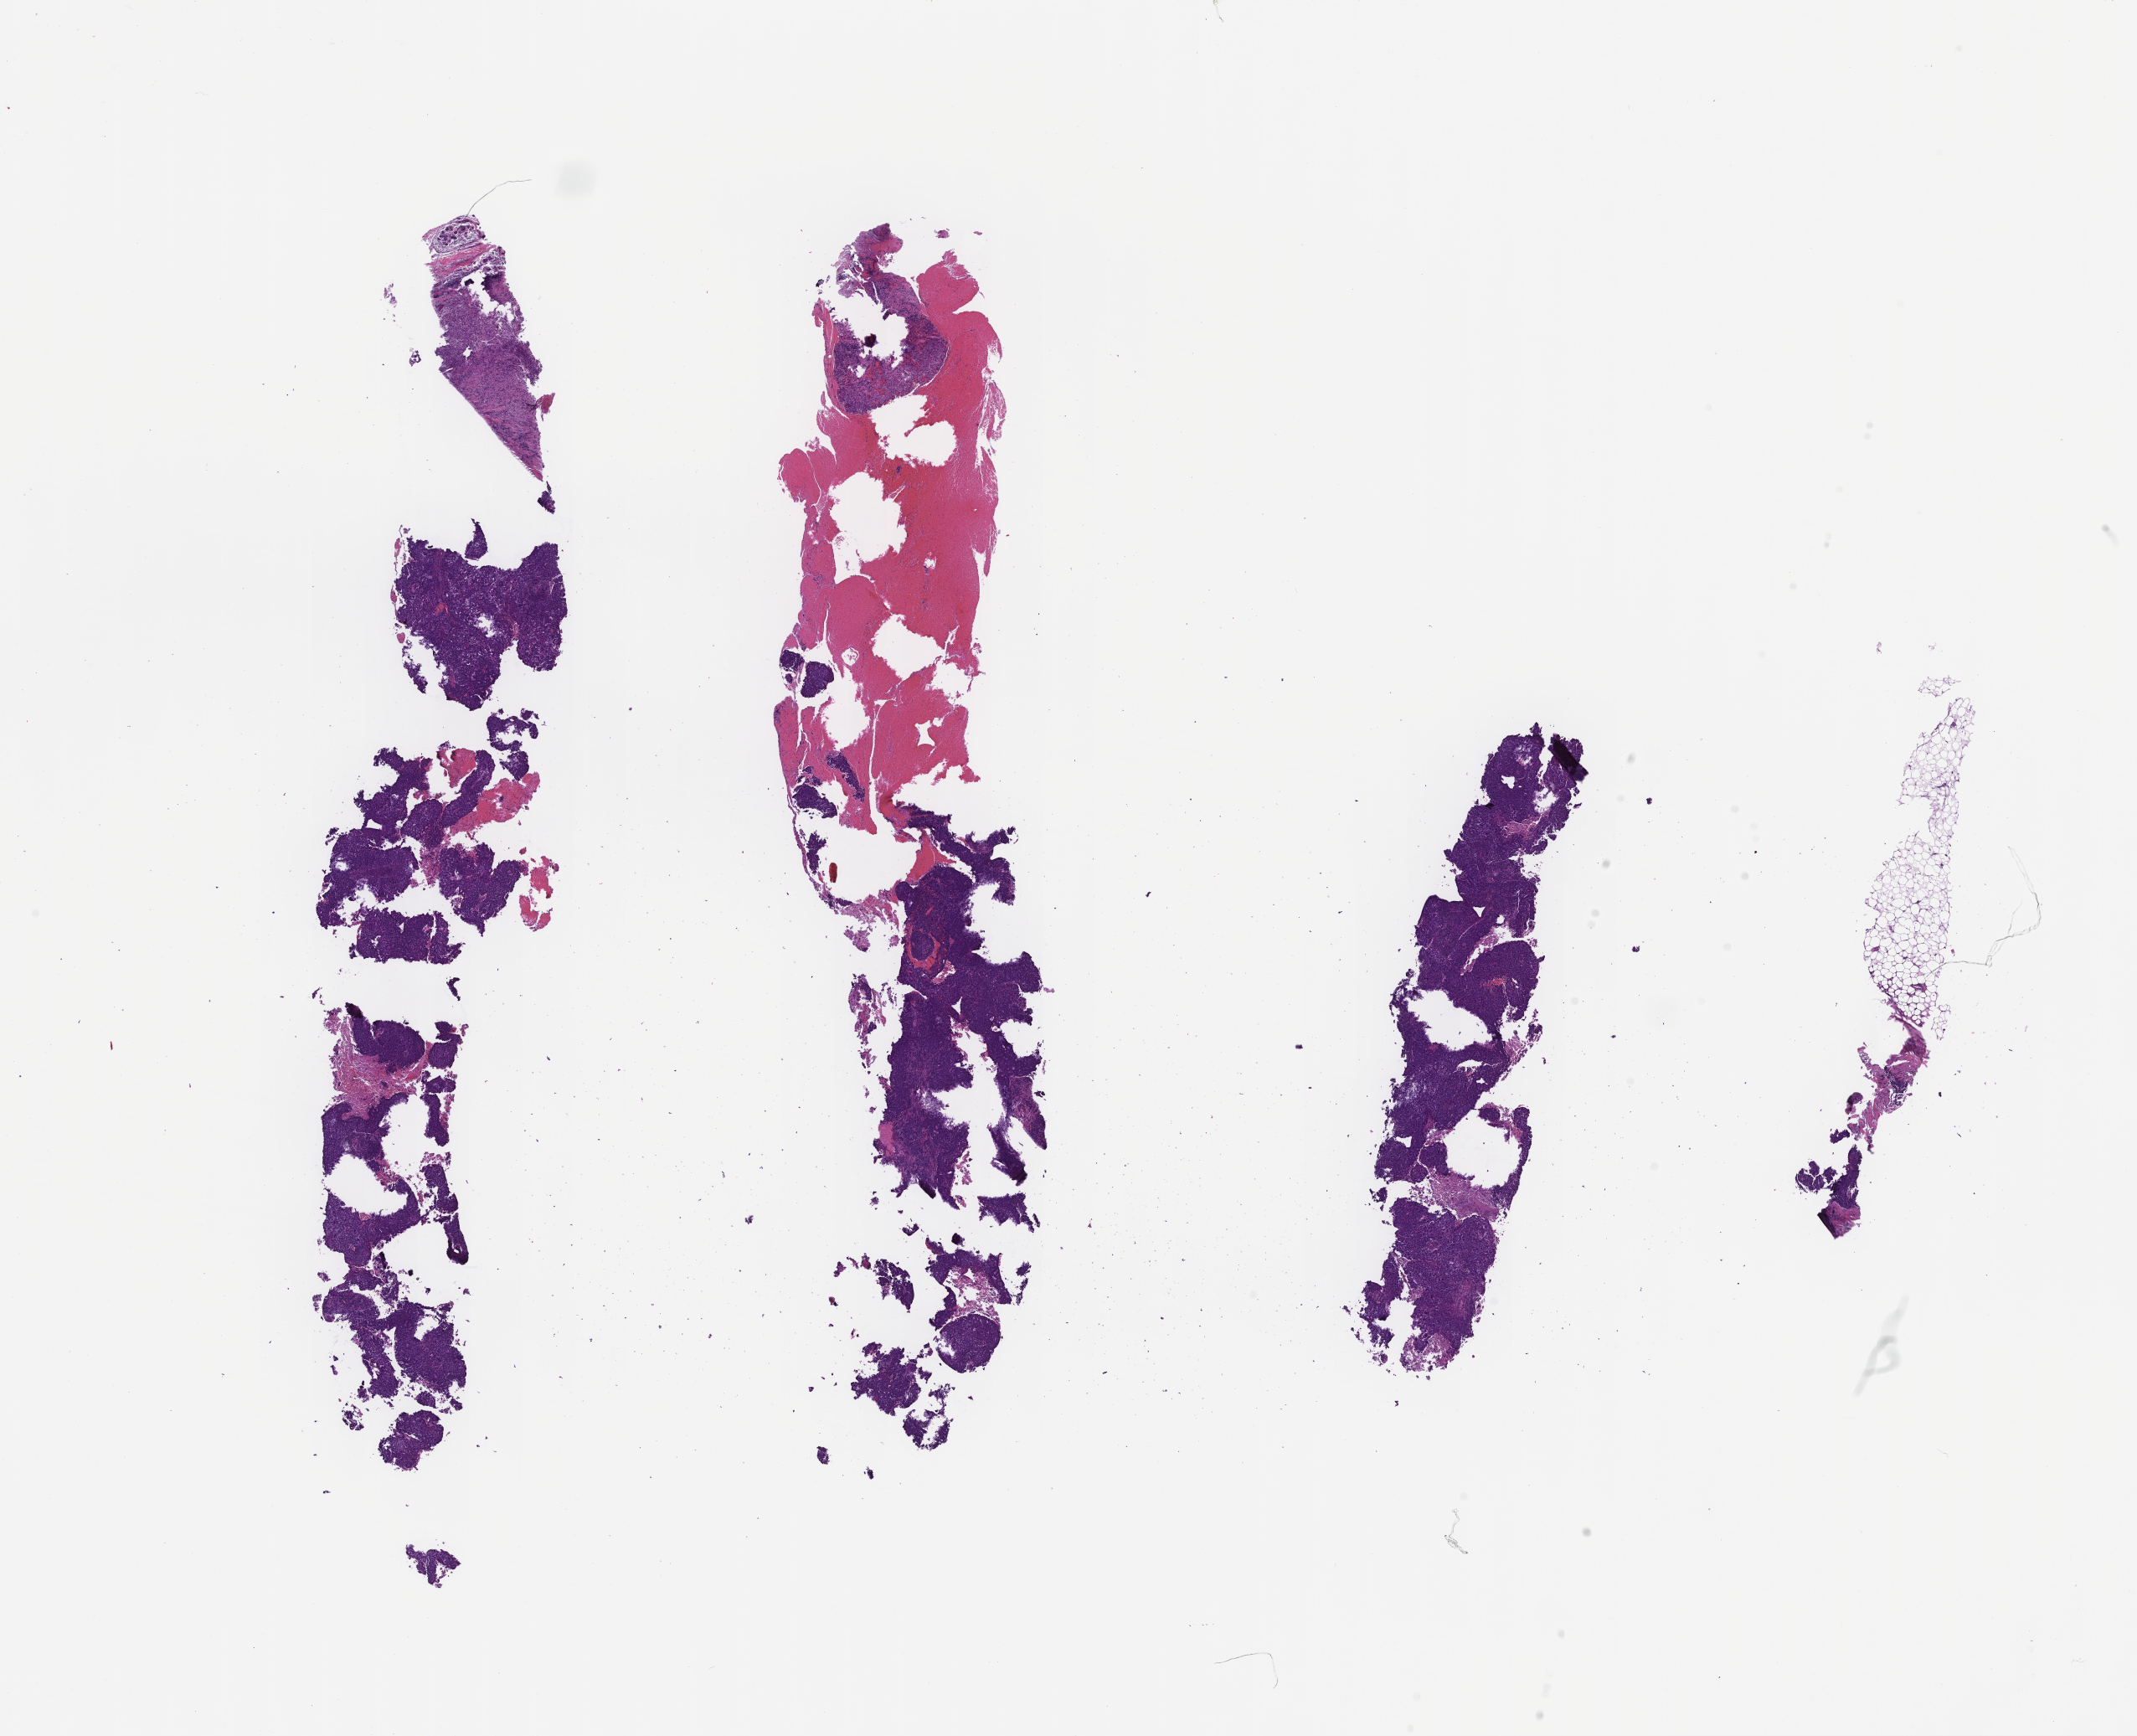
Haematoxylin and eosin whole-slide image, low-resolution overview of the scanned area, about 20.6 x 16.7 mm. Formalin-fixed paraffin-embedded section. Site: breast. Specimen time point: archival tissue. Female patient.
* this section: primary tumor
* diagnosis: Invasive Breast Carcinoma